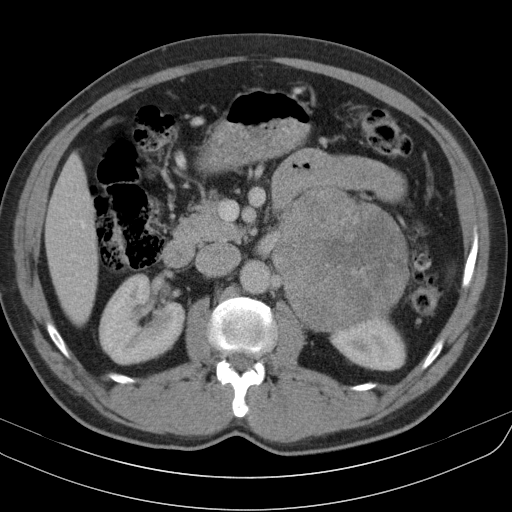
Contrast-enhanced abdominal CT, one axial slice. Slice 61 of 91 in the series (ordered by position). Reconstruction kernel B31s. Intravenous contrast given. Soft-tissue window (W 400 / L 40 HU). 5 mm slice thickness. 512 × 512 image matrix, field of view 370 × 370 mm. Male patient, age 51 years. Case-level facts recorded for this patient, not image findings: diagnosis: adrenocortical carcinoma; tumour side: left adrenal.
Annotated regions visible in this slice (semi-automatic segmentation, software-assisted and operator-edited):
- mass: bounding box [x1, y1, x2, y2] px = [275, 188, 408, 329]